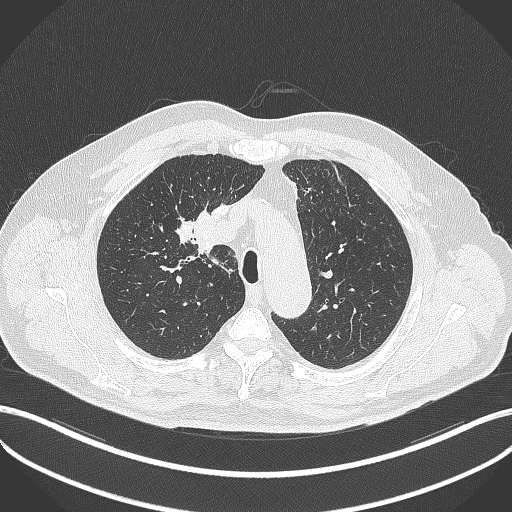
Chest CT, one axial slice; slice 295 of 411 in the series (ordered by position); reconstruction kernel B70f; 120 kVp; lung window (W 1500 / L -600 HU); 1 mm slice thickness; 512 × 512 image matrix. Male patient, age 60 years. From the clinical record (not read from this slice): clinical TNM (as recorded): T1b N1 M0.
Outlined on this slice (bounding box drawn by a radiologist):
- lung tumour (recorded histology: squamous cell carcinoma): bounding box [x1, y1, x2, y2] px = [192, 202, 219, 259]